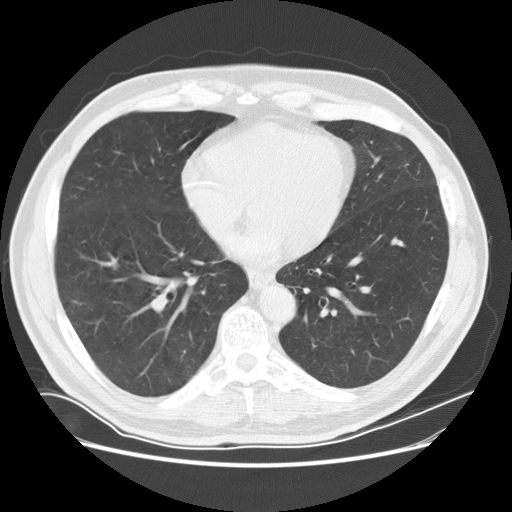
Axial slice from a low-dose chest CT screening exam. First (baseline) screen. Lung window (W 1500 / L -600 HU). 512 × 512 image matrix, field of view 380 × 380 mm. Male participant, aged 72 years at enrolment.
Lesion marked by an expert reader, bounding box <52,289,90,322> (left, top, right, bottom; pixels). Screening reader's record for this exam (one nodule recorded; not confirmed to be the boxed lesion): non-calcified nodule or mass ≥4 mm, right lower lobe, 13 × 8 mm, poorly defined margins, soft tissue attenuation.